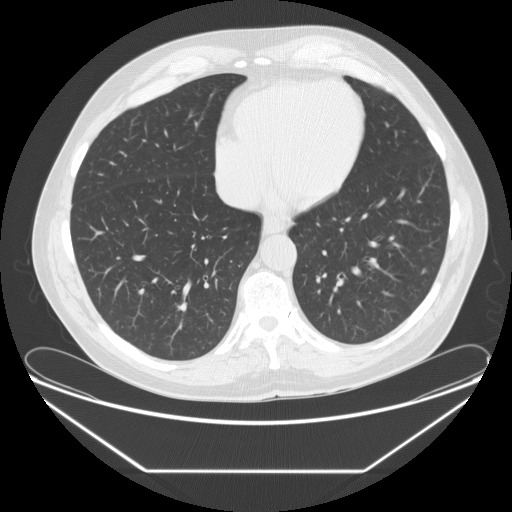
Axial slice from a low-dose chest CT screening exam; baseline screening round; lung window (W 1500 / L -600 HU); standard (soft-tissue) reconstruction kernel (STANDARD); 120 kVp; slice 173 of 261 in the series; 512 × 512 image matrix. Male, age 67 years at enrolment. Current smoker at enrolment.
- Expert reader's lesion annotation, bounding box (x1, y1, x2, y2) in pixels: (414, 256, 436, 281).
- Reader record for this screening exam (exam-level; its link to the box is not recorded): non-calcified nodule or mass ≥4 mm, left lower lobe, 4 × 4 mm, poorly defined margins, soft tissue attenuation.
- Later outcome: lung cancer diagnosed 623 days after this screen (after the second annual screen) — adenocarcinoma, NOS, left lower lobe, moderately differentiated (G2), stage IIA (AJCC 6th edition), 6 mm at pathology.